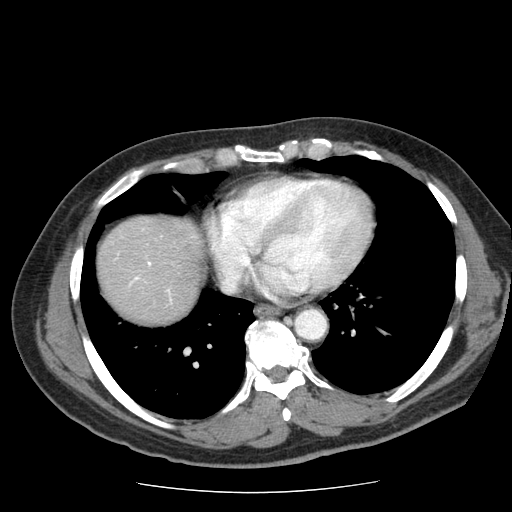
Contrast-enhanced abdominal CT (liver protocol), one axial slice; position 71 of 85 along the scan axis; reconstruction kernel STANDARD; 120 kVp; soft-tissue window (W 400 / L 40 HU); 512 × 512 image matrix, field of view 360 × 360 mm. Case-level facts recorded for this patient, not image findings: diagnosis: hepatocellular carcinoma (patient treated with transarterial chemoembolisation; whether this scan precedes or follows treatment is not stated here); TNM stage (as recorded): Stage-IIIA; Child-Pugh class: A; tumour differentiation: well differentiated; tumour nodularity: multinodular.
Annotated regions visible in this slice (semi-automatically segmented with operator editing):
- liver parenchyma outside the tumour (the mass and vessels are separate outlines, so this box may not span the whole liver): box from (x=98, y=216) to (x=202, y=322) px
- liver vessels: (x=134, y=262)–(x=169, y=292)